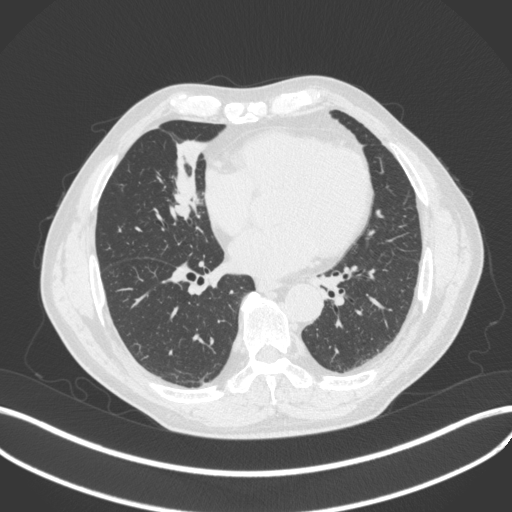
Chest CT, one axial slice; 120 kVp; lung window (W 1500 / L -600 HU); 1 mm slice thickness; 512 × 512 image matrix, field of view 400 × 400 mm. Male patient, age 61 years. Case-level facts recorded for this patient, not image findings: clinical TNM (as recorded): T2b N1 M0.
Outlined on this slice (rectangle marked by the reading radiologist):
- lung tumour (recorded histology: squamous cell carcinoma): bounding box [x1, y1, x2, y2] px = [161, 165, 208, 230]